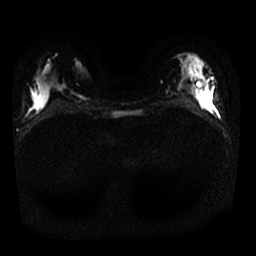
Breast MRI, one axial slice; position 10 of 25 along the scan axis; diffusion-weighted series; image 2 of 4 stored at this slice position (different b-values; order by instance number); 1.5 T; 4 mm slice thickness; 256 × 256 image matrix. Female patient.
Annotated regions visible in this slice (expert manual segmentation):
- tumour on diffusion-weighted imaging: bounding box [x1, y1, x2, y2] px = [203, 87, 209, 96]